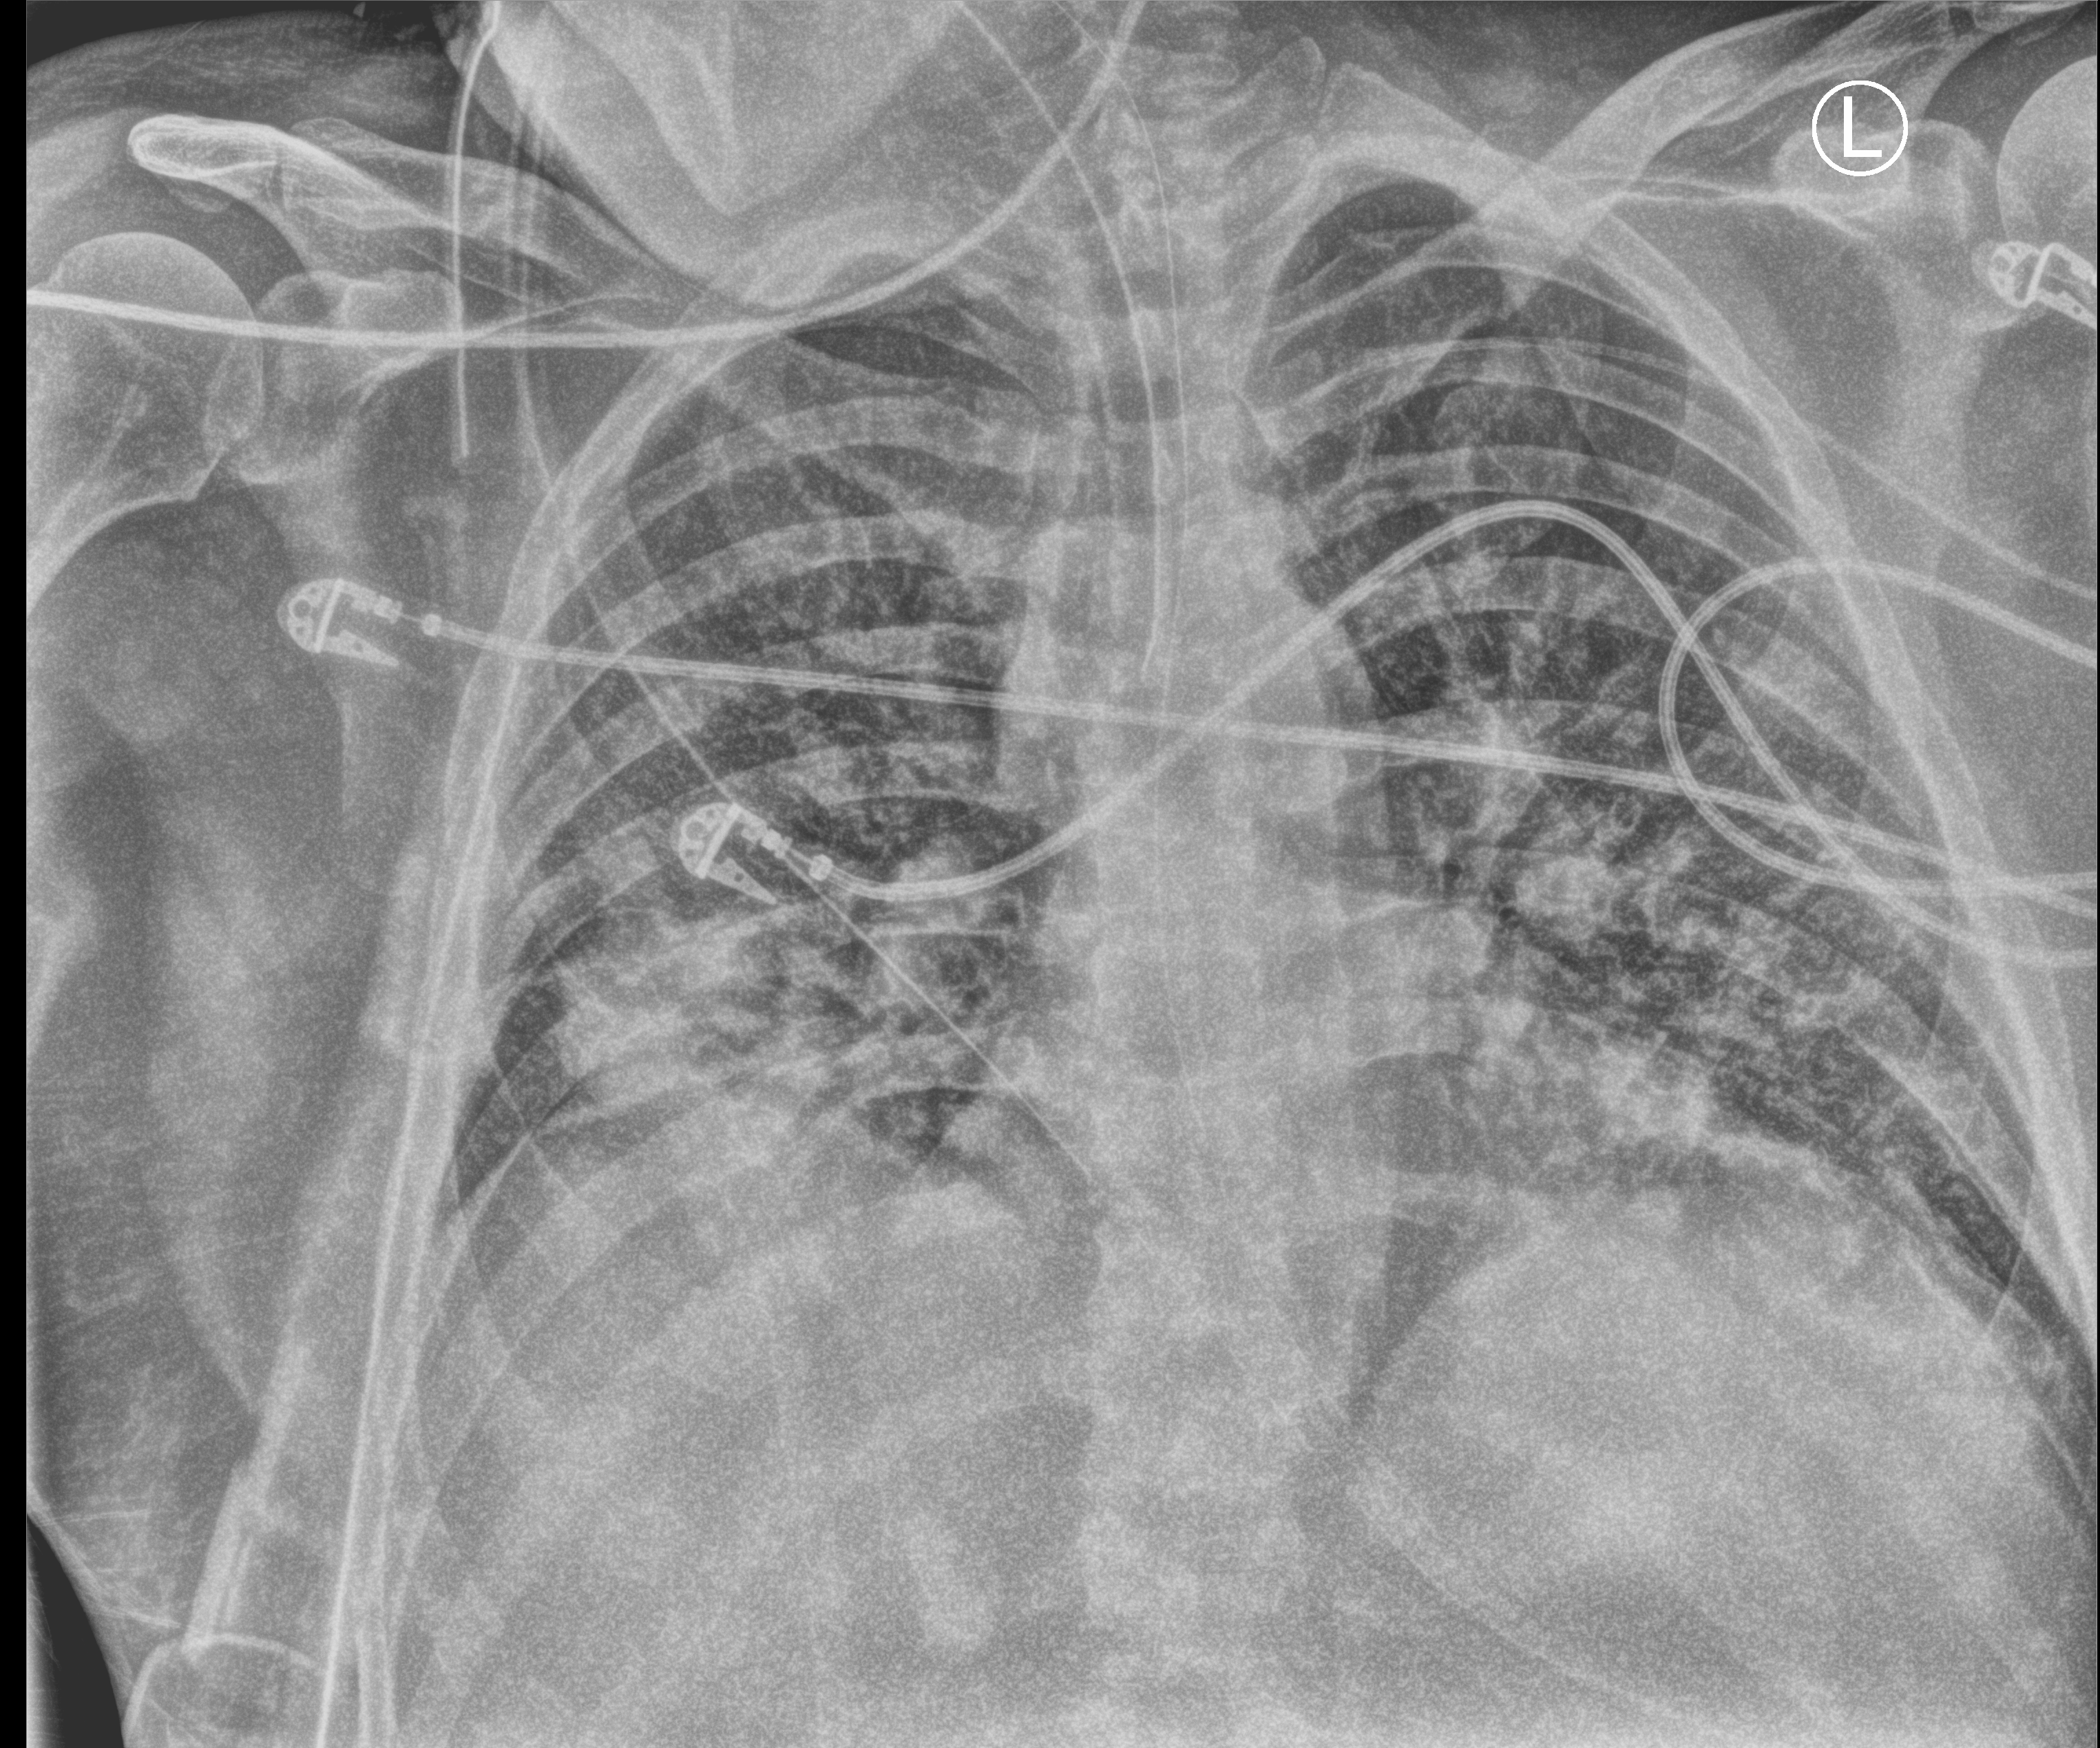
Portable chest radiograph, anteroposterior (AP) projection. Male patient hospitalised with COVID-19, age 18–59 years.
Hospital-stay facts (about this admission, not read from this image; timing relative to this image not recorded): length of hospital stay: 80 days; mechanically ventilated during this hospital stay: yes; other chronic lung disease (admission record): no.